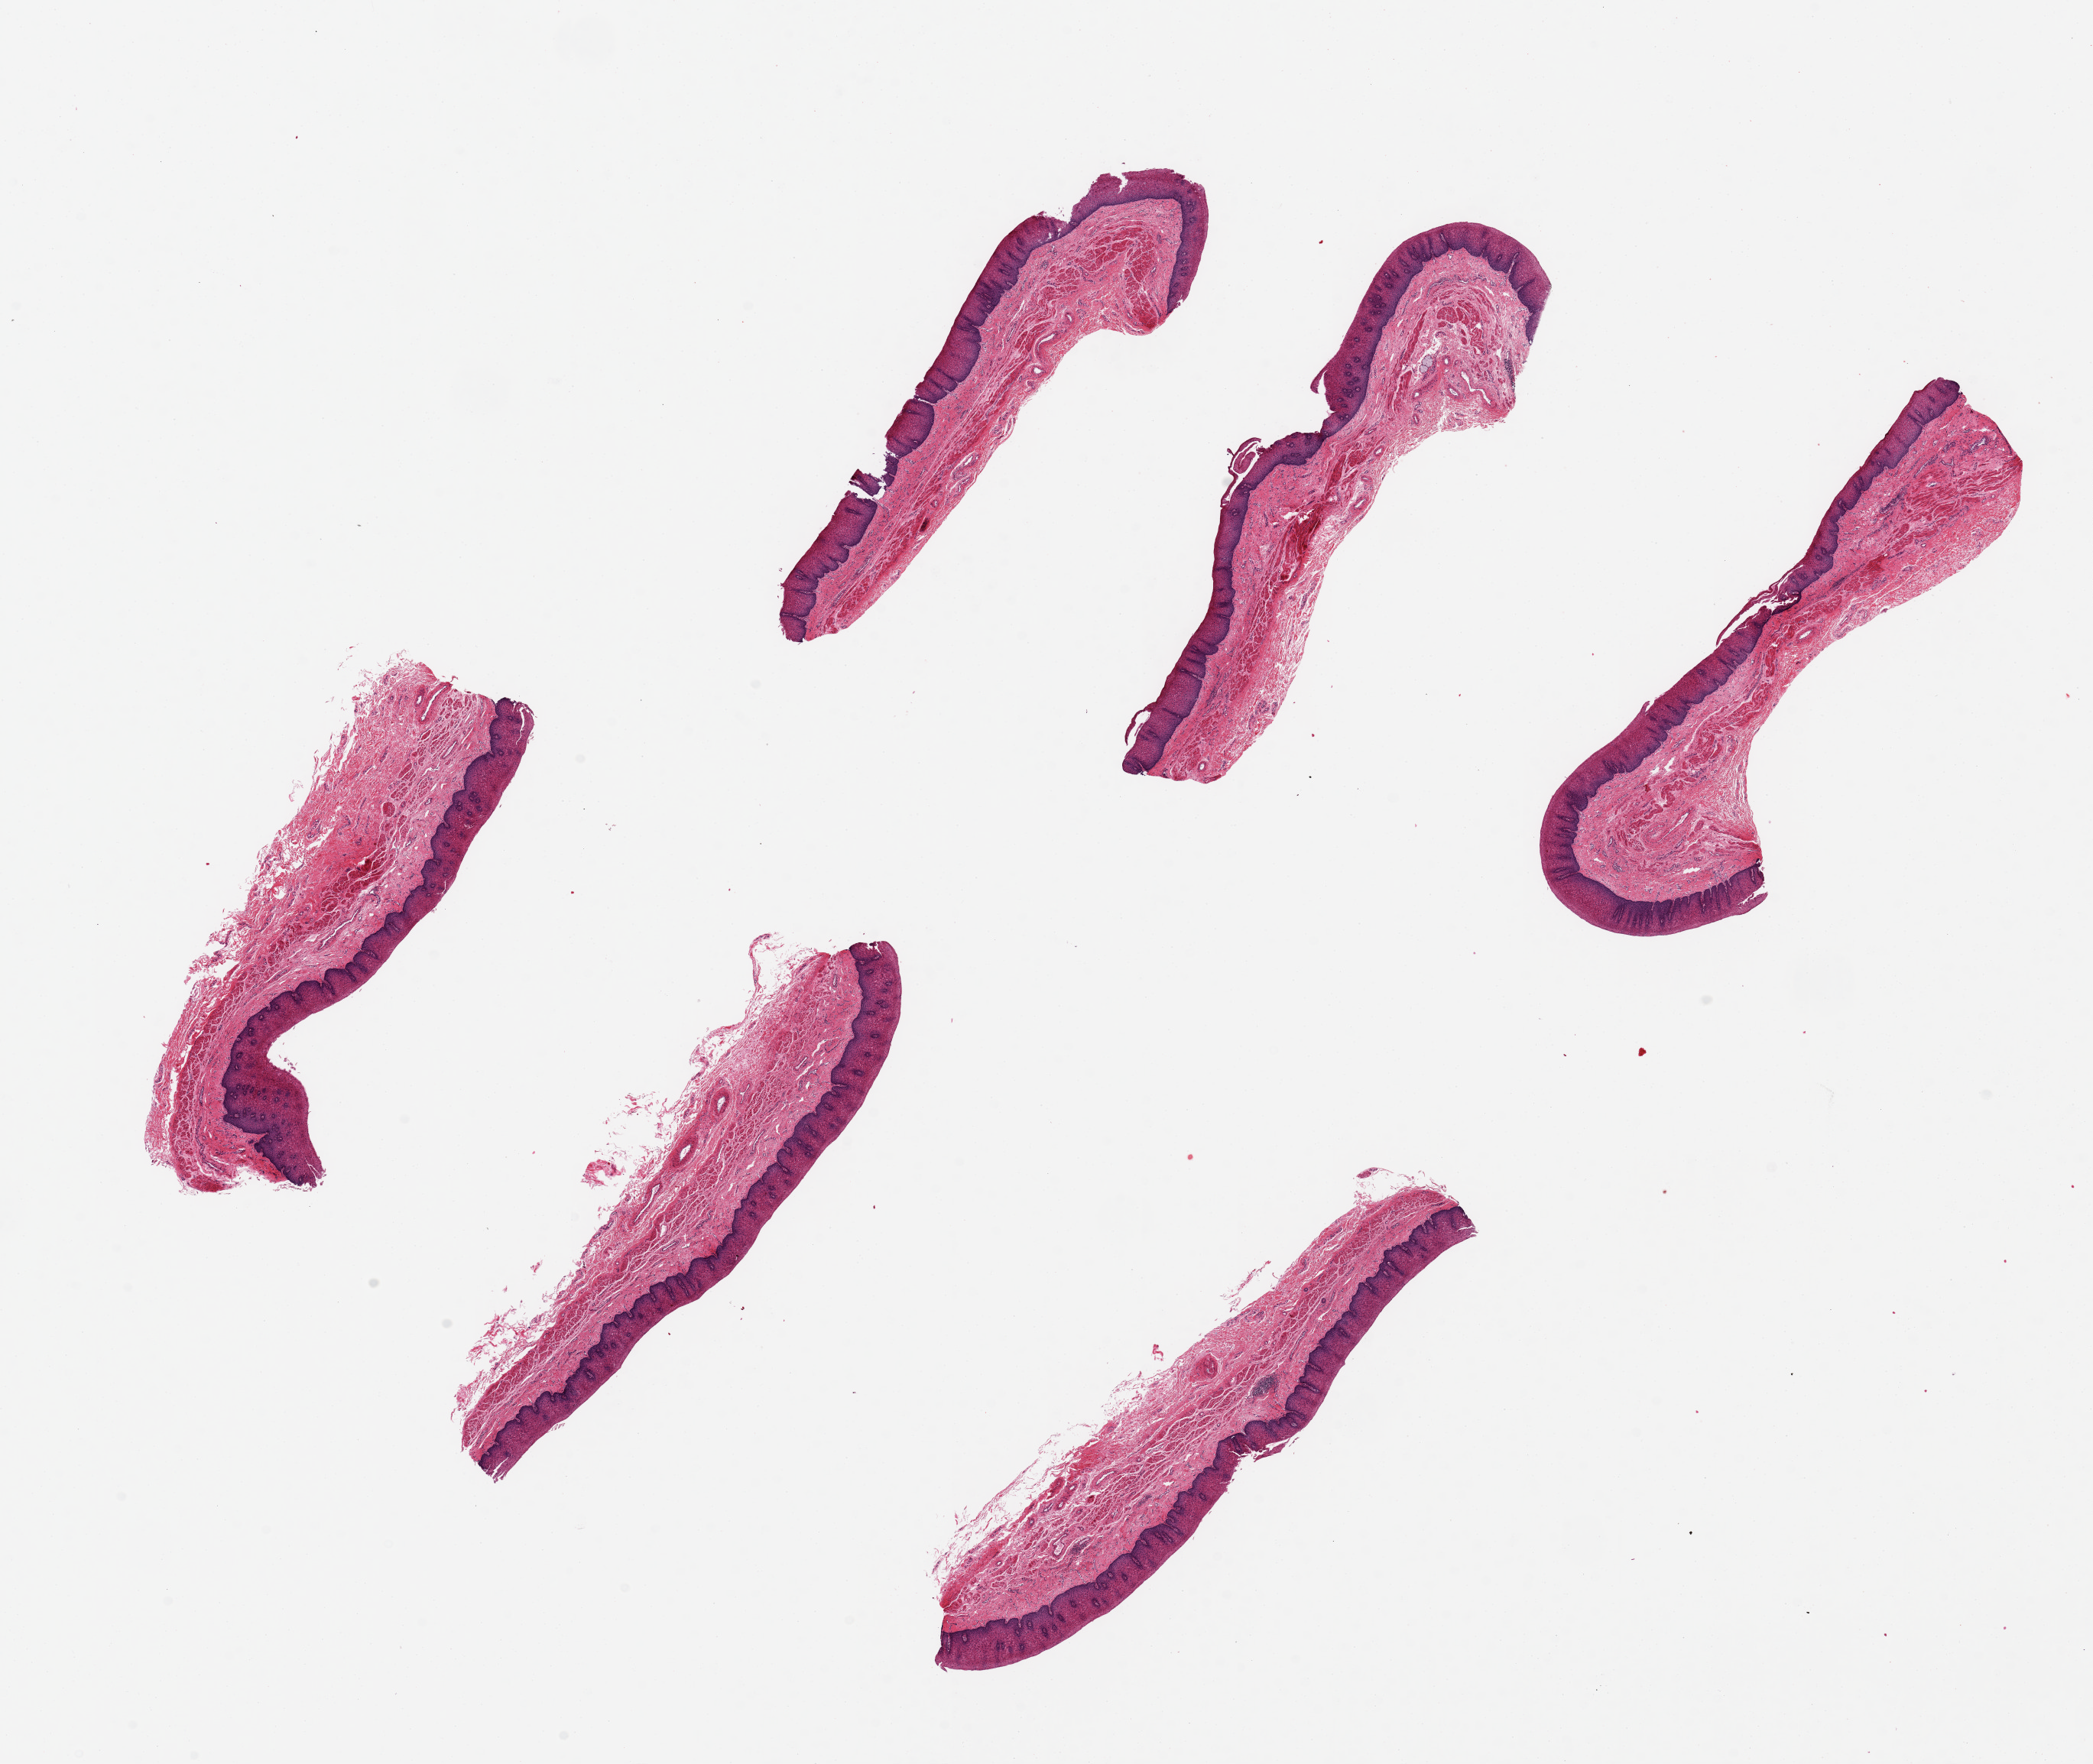
Digitized hematoxylin and eosin (H&E)-stained section, low-resolution overview of the scanned area, about 21.7 x 18.3 mm, PAXgene-fixed, paraffin-embedded tissue, sampled site (target tissue): esophageal mucous membrane, tissue donor sample. Donor sex: male.
Reviewer comment on this tissue sample: 6 pieces ~6x1.5mm, Squamous mucosa is ~10% thickness.